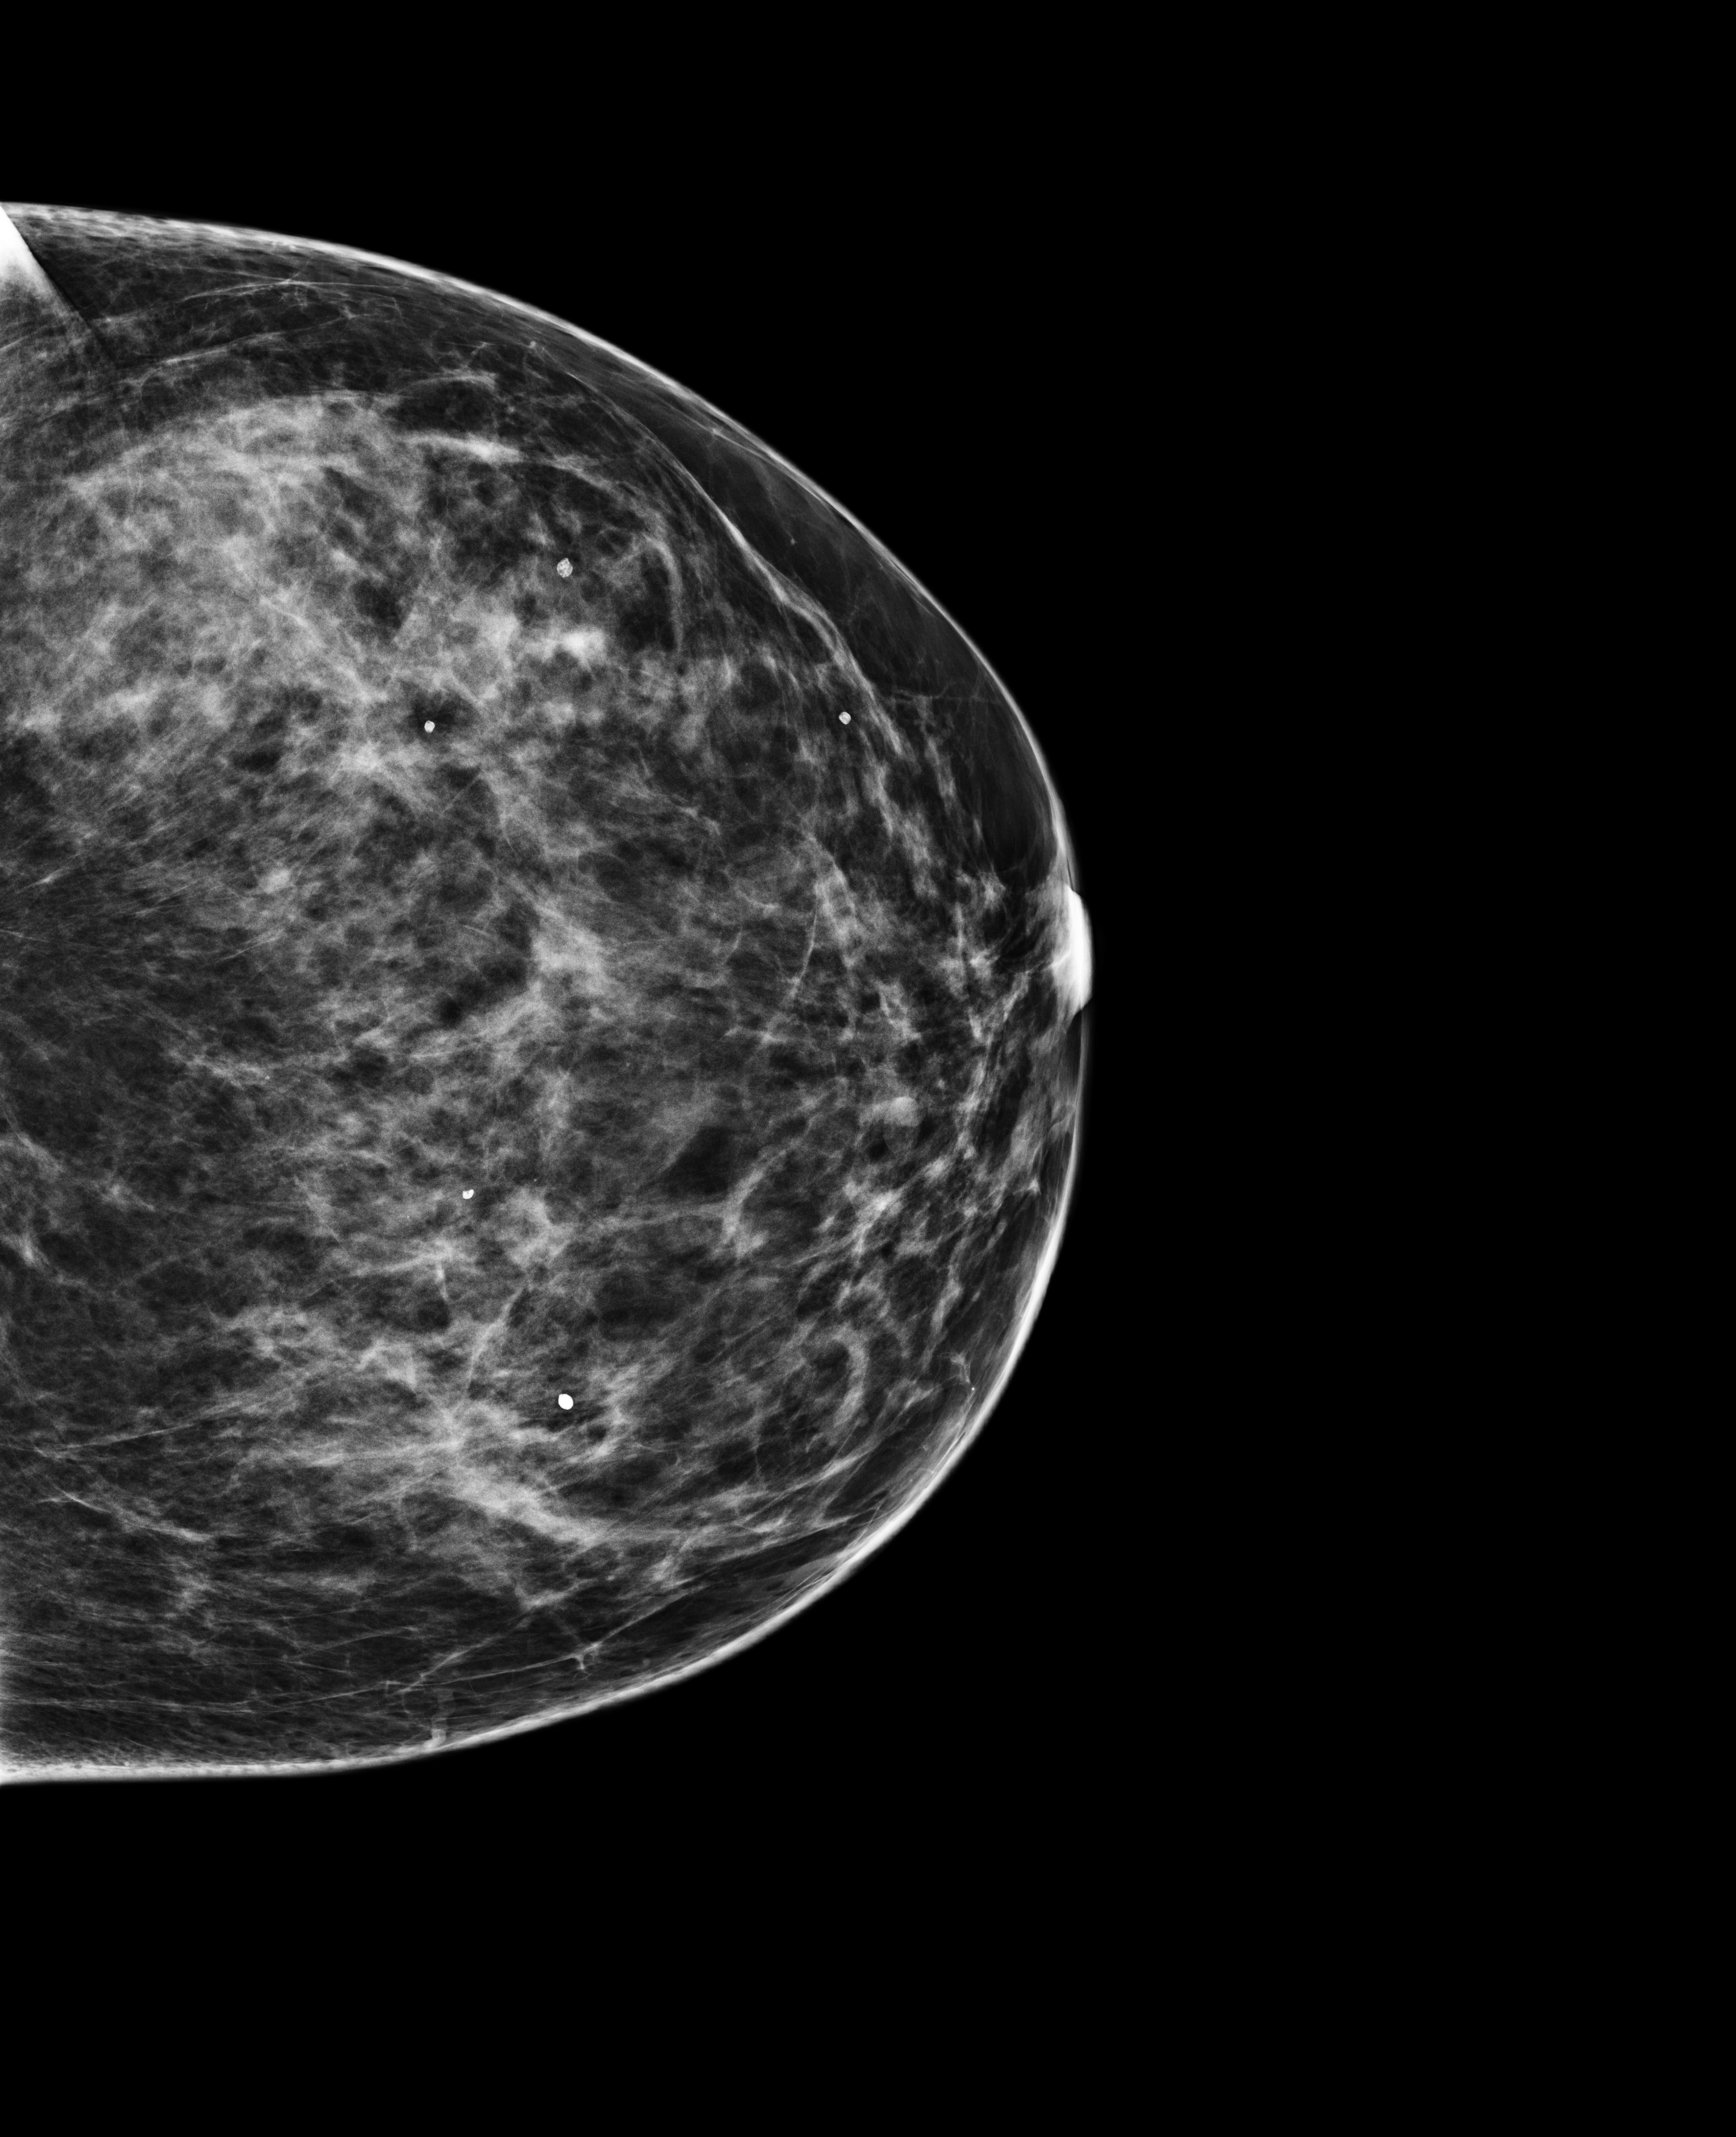
Full-field digital mammogram (FFDM); left breast; CC view; screening examination; compressed breast thickness 84 mm. Patient aged 44 years (female).
BI-RADS breast density category at the screening exam (both breasts, scale 1–4): 3. Final BI-RADS category for the screening round (tomosynthesis exam, both breasts): category 2. Recall: no recall after this screen.